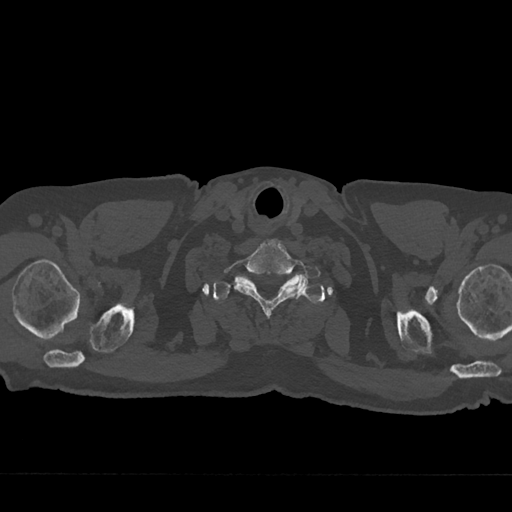
CT including the spine, one axial slice. Position 682 of 797 along the scan axis. 120 kVp. Bone window (W 1800 / L 400 HU). 0.5 mm slice thickness. 512 × 512 image matrix, field of view 377 × 377 mm. Male patient, age 75 years. Case-level facts recorded for this patient, not image findings: primary cancer: renal; vertebrae with lytic lesions (as recorded): T4.
Annotated regions visible in this slice (semi-automatically segmented with operator editing):
- T1 vertebra: bounding box [x1, y1, x2, y2] px = [213, 276, 312, 301]